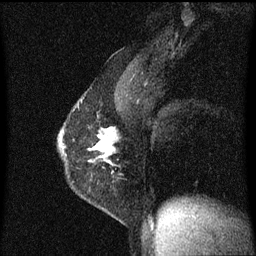
Breast MRI (dynamic contrast-enhanced), one sagittal slice. Slice 39 of 60 in the series (ordered by position). Dynamic contrast-enhanced series, image 2 of 3 at this slice position (ordered by acquisition). 1.5 T. TE 4.2 ms, TR 8.4 ms. 256 × 256 image matrix. Female patient, age 40 years.
Outlined on this slice (semi-automatic segmentation, software-assisted and operator-edited):
- analysis volume of interest (the breast-tissue region the enhancement analysis was run in; not a lesion): box from (x=58, y=114) to (x=119, y=191) px
- tumour enhancement mask (voxels above the 70 % enhancement threshold inside the analysis volume of interest): (x=58, y=128)–(x=115, y=165)